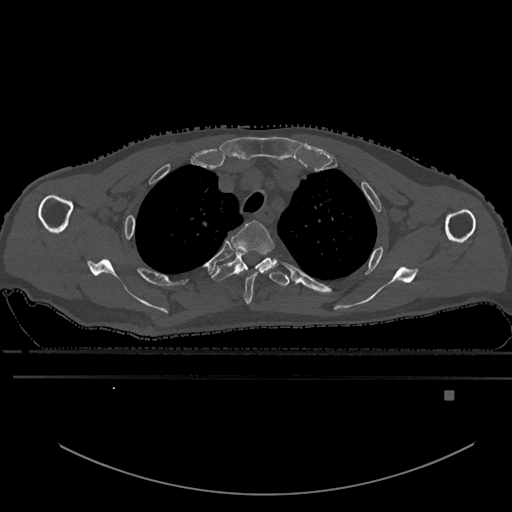
CT including the spine, one axial slice; position 472 of 969 along the scan axis; bone window (W 1800 / L 400 HU); 0.5 mm slice thickness; 512 × 512 image matrix, field of view 456 × 456 mm. Patient: male, 82 years. From the clinical record (not read from this slice): primary cancer: prostate; vertebrae with lytic lesions (as recorded): T11, T9, T8, T2.
Structures marked on this image (semi-automatically segmented with operator editing):
- T2 vertebra: box from (x=231, y=220) to (x=276, y=304) px
- T3 vertebra: (x=211, y=251)–(x=289, y=287)